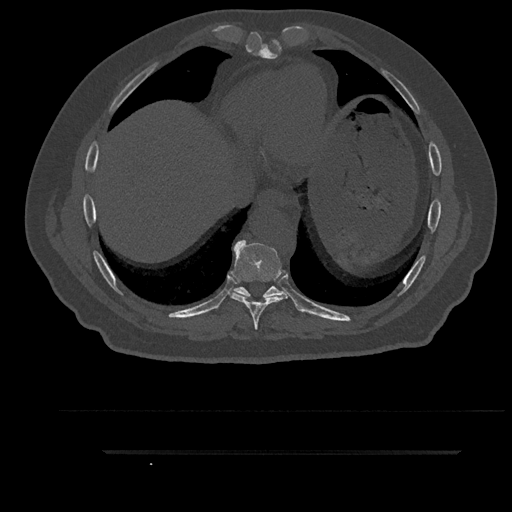
CT including the spine, one axial slice. Slice 454 of 797 in the series (ordered by position). Reconstruction kernel Br40s/3. Bone window (W 1800 / L 400 HU). 0.5 mm slice thickness. 512 × 512 image matrix, field of view 432 × 432 mm. Male patient, age 63 years. From the clinical record (not read from this slice): primary cancer: renal; vertebrae with lytic lesions (as recorded): T8.
Outlined on this slice (semi-automatic segmentation, software-assisted and operator-edited):
- T8 vertebra: bounding box (x1, y1, x2, y2) in pixels: (230, 240, 287, 329)
- T9 vertebra: (232, 286, 284, 298)